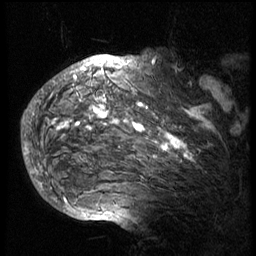
Breast MRI (dynamic contrast-enhanced), one sagittal slice. Slice 56 of 74 in the series (ordered by position). 3 images stored at this slice position (order not interpretable as contrast timing). 1.5 T. TE 4.2 ms, TR 8.9 ms. 256 × 256 image matrix. Female patient, age 57 years. Case-level facts recorded for this patient, not image findings: setting: breast cancer imaged before/during neoadjuvant chemotherapy; receptor status: HER2-positive.
Outlined on this slice (semi-automatic segmentation, software-assisted and operator-edited):
- analysis volume of interest (the breast-tissue region the enhancement analysis was run in; not a lesion): bounding box [x1, y1, x2, y2] px = [40, 62, 239, 175]
- tumour enhancement mask (voxels above the 140 % enhancement threshold inside the analysis volume of interest): [40, 62, 211, 173]